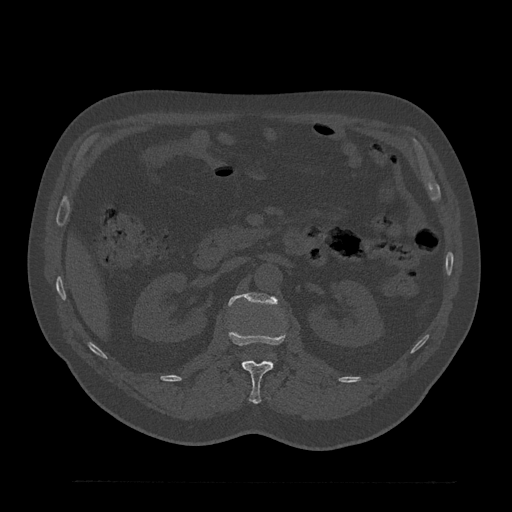
CT including the spine, one axial slice; position 145 of 797 along the scan axis; reconstruction kernel Br40s/3; 120 kVp; bone window (W 1800 / L 400 HU); 0.5 mm slice thickness; 512 × 512 image matrix, field of view 430 × 430 mm. Patient: male, 61 years. Case-level facts recorded for this patient, not image findings: primary cancer: prostate.
Annotated regions visible in this slice (semi-automatic segmentation, software-assisted and operator-edited):
- L1 vertebra: bounding box (x1, y1, x2, y2) in pixels: (228, 329, 286, 404)
- L2 vertebra: (228, 293, 278, 306)